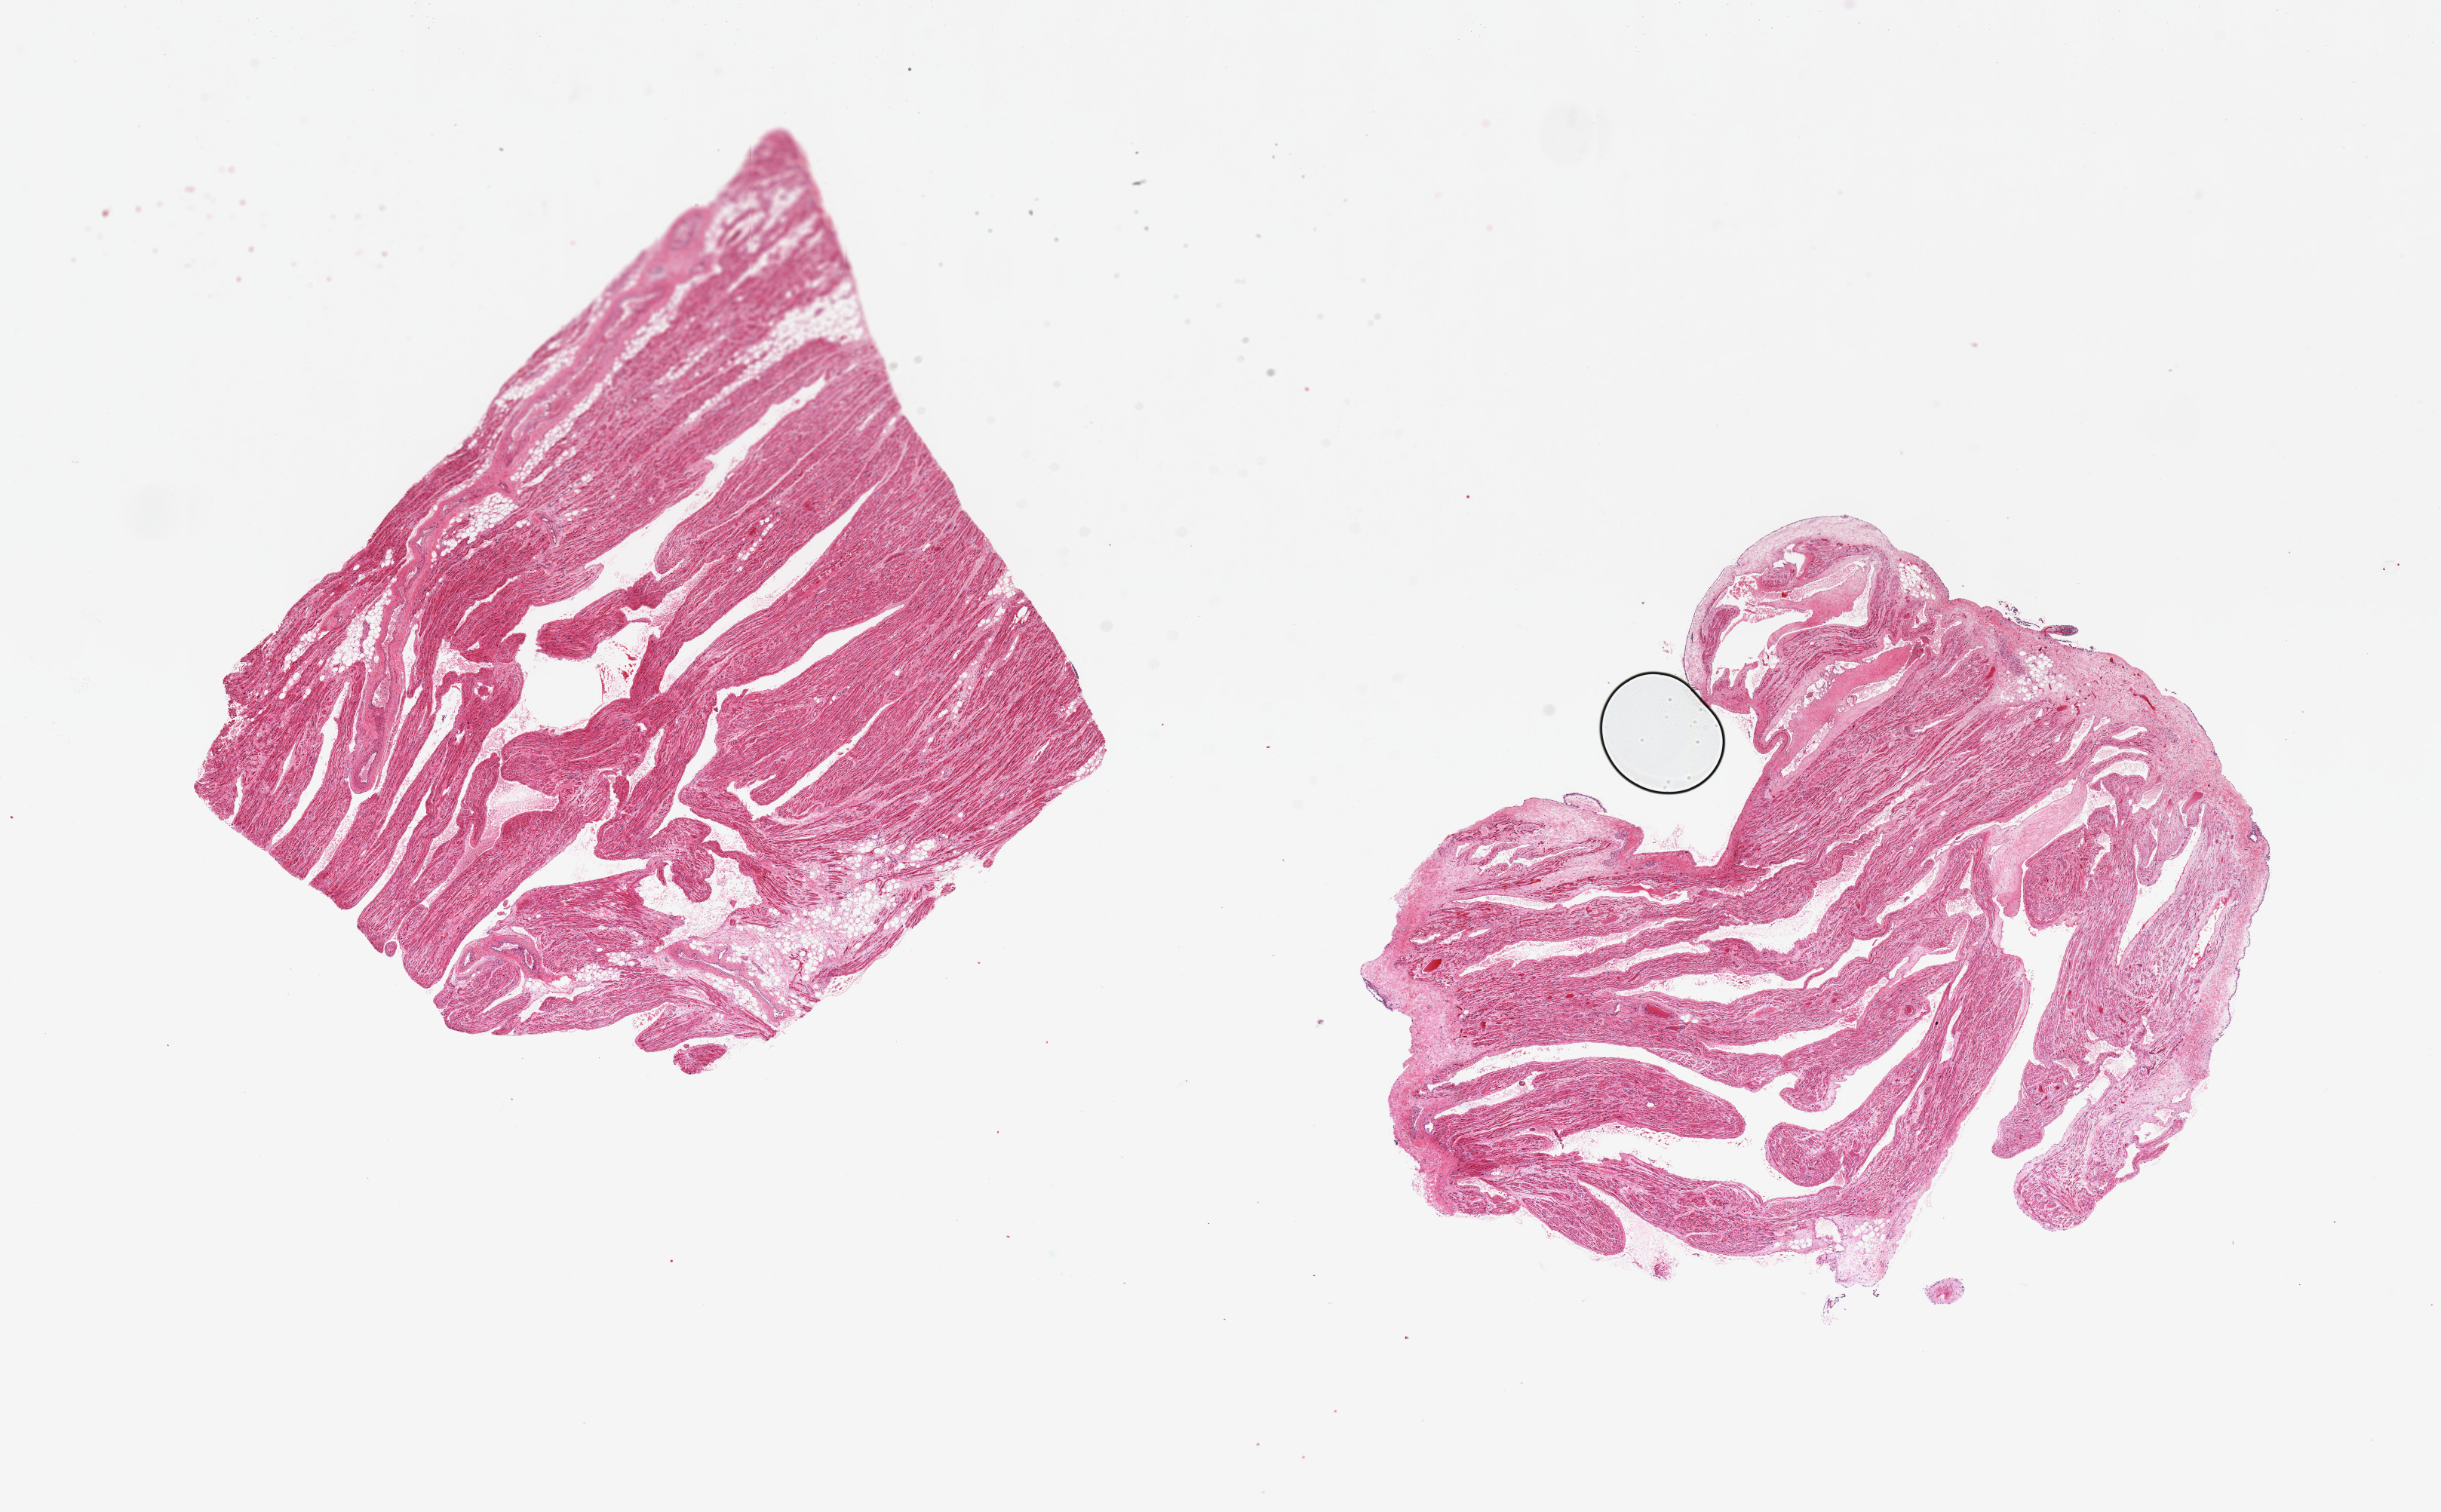
Digitized haematoxylin and eosin-stained section, whole scanned area (about 25.6 x 15.9 mm, slide scanned at 20x) shown as a low-resolution overview. PAXgene-fixed paraffin-embedded (PFPE) section. Section of auricular appendage (target tissue). Donor tissue sample.
Reviewer comment on this tissue sample: 2 pieces, 9x7 & 10x8mm; 0.5 mm thick epicardium on one.